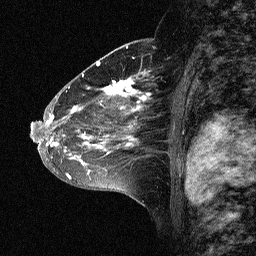
Breast MRI (dynamic contrast-enhanced), one sagittal slice. Slice 38 of 64 in the series (ordered by position). Dynamic contrast-enhanced study with each time point stored as its own series, time point 2 of 3 at this slice position (early post-contrast, ordered by acquisition time). 1.5 T. TE 4.5 ms, TR 11 ms. 2.06 mm slice thickness. 256 × 256 image matrix, field of view 200 × 200 mm. Female patient, age 46 years. Case-level facts recorded for this patient, not image findings: setting: breast cancer imaged before/during neoadjuvant chemotherapy; receptor status: HER2-positive.
Structures marked on this image (semi-automatically segmented with operator editing):
- analysis volume of interest (the breast-tissue region the enhancement analysis was run in; not a lesion): bounding box [x1, y1, x2, y2] px = [43, 72, 164, 177]
- tumour enhancement mask (voxels above the 90 % enhancement threshold inside the analysis volume of interest): [45, 72, 151, 177]